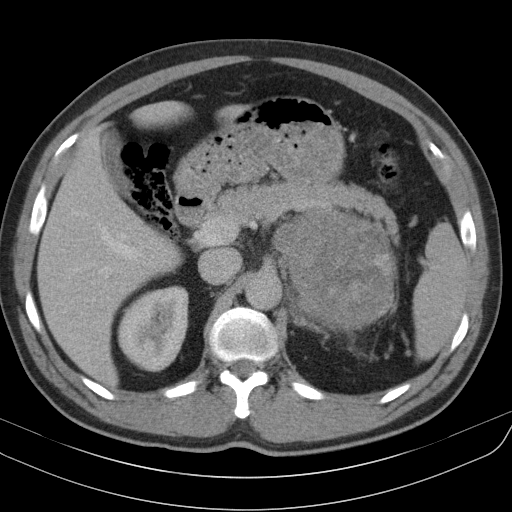
Contrast-enhanced abdominal CT, one axial slice; position 68 of 91 along the scan axis; intravenous contrast given; soft-tissue window (W 400 / L 40 HU); 5 mm slice thickness; 512 × 512 image matrix, field of view 370 × 370 mm. Patient: male, 51 years. Case-level facts recorded for this patient, not image findings: diagnosis: adrenocortical carcinoma; tumour side: left adrenal; tumour size at pathology: 18 cm; Ki-67 index: 40 %; stage (as recorded): 3.
Annotated regions visible in this slice (semi-automatic segmentation, software-assisted and operator-edited):
- mass: bounding box [x1, y1, x2, y2] px = [274, 211, 393, 329]